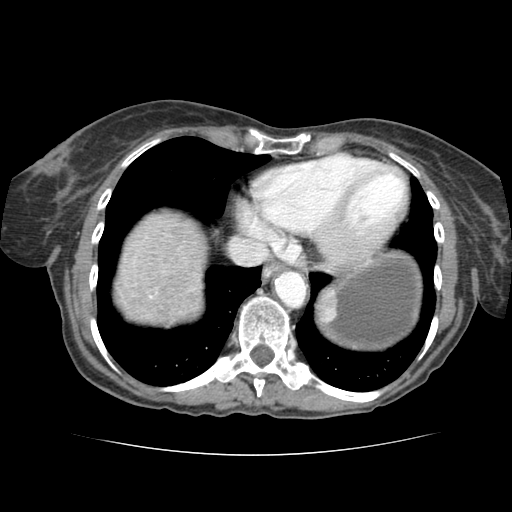
Contrast-enhanced abdominal CT (liver protocol), one axial slice; slice 73 of 77 in the series (ordered by position); reconstruction kernel STANDARD; 120 kVp; soft-tissue window (W 400 / L 40 HU); 512 × 512 image matrix, field of view 340 × 340 mm. From the clinical record (not read from this slice): diagnosis: hepatocellular carcinoma (patient treated with transarterial chemoembolisation; whether this scan precedes or follows treatment is not stated here); TNM stage (as recorded): Stage-I; Child-Pugh class: A; tumour differentiation: well differentiated; tumour size: 7.6 cm.
Annotated regions visible in this slice (semi-automatic segmentation, software-assisted and operator-edited):
- abdominal aorta: bounding box (x1, y1, x2, y2) in pixels: (274, 270, 306, 306)
- liver parenchyma outside the tumour (the mass and vessels are separate outlines, so this box may not span the whole liver): (122, 220, 195, 306)
- liver vessels: (155, 277, 159, 284)